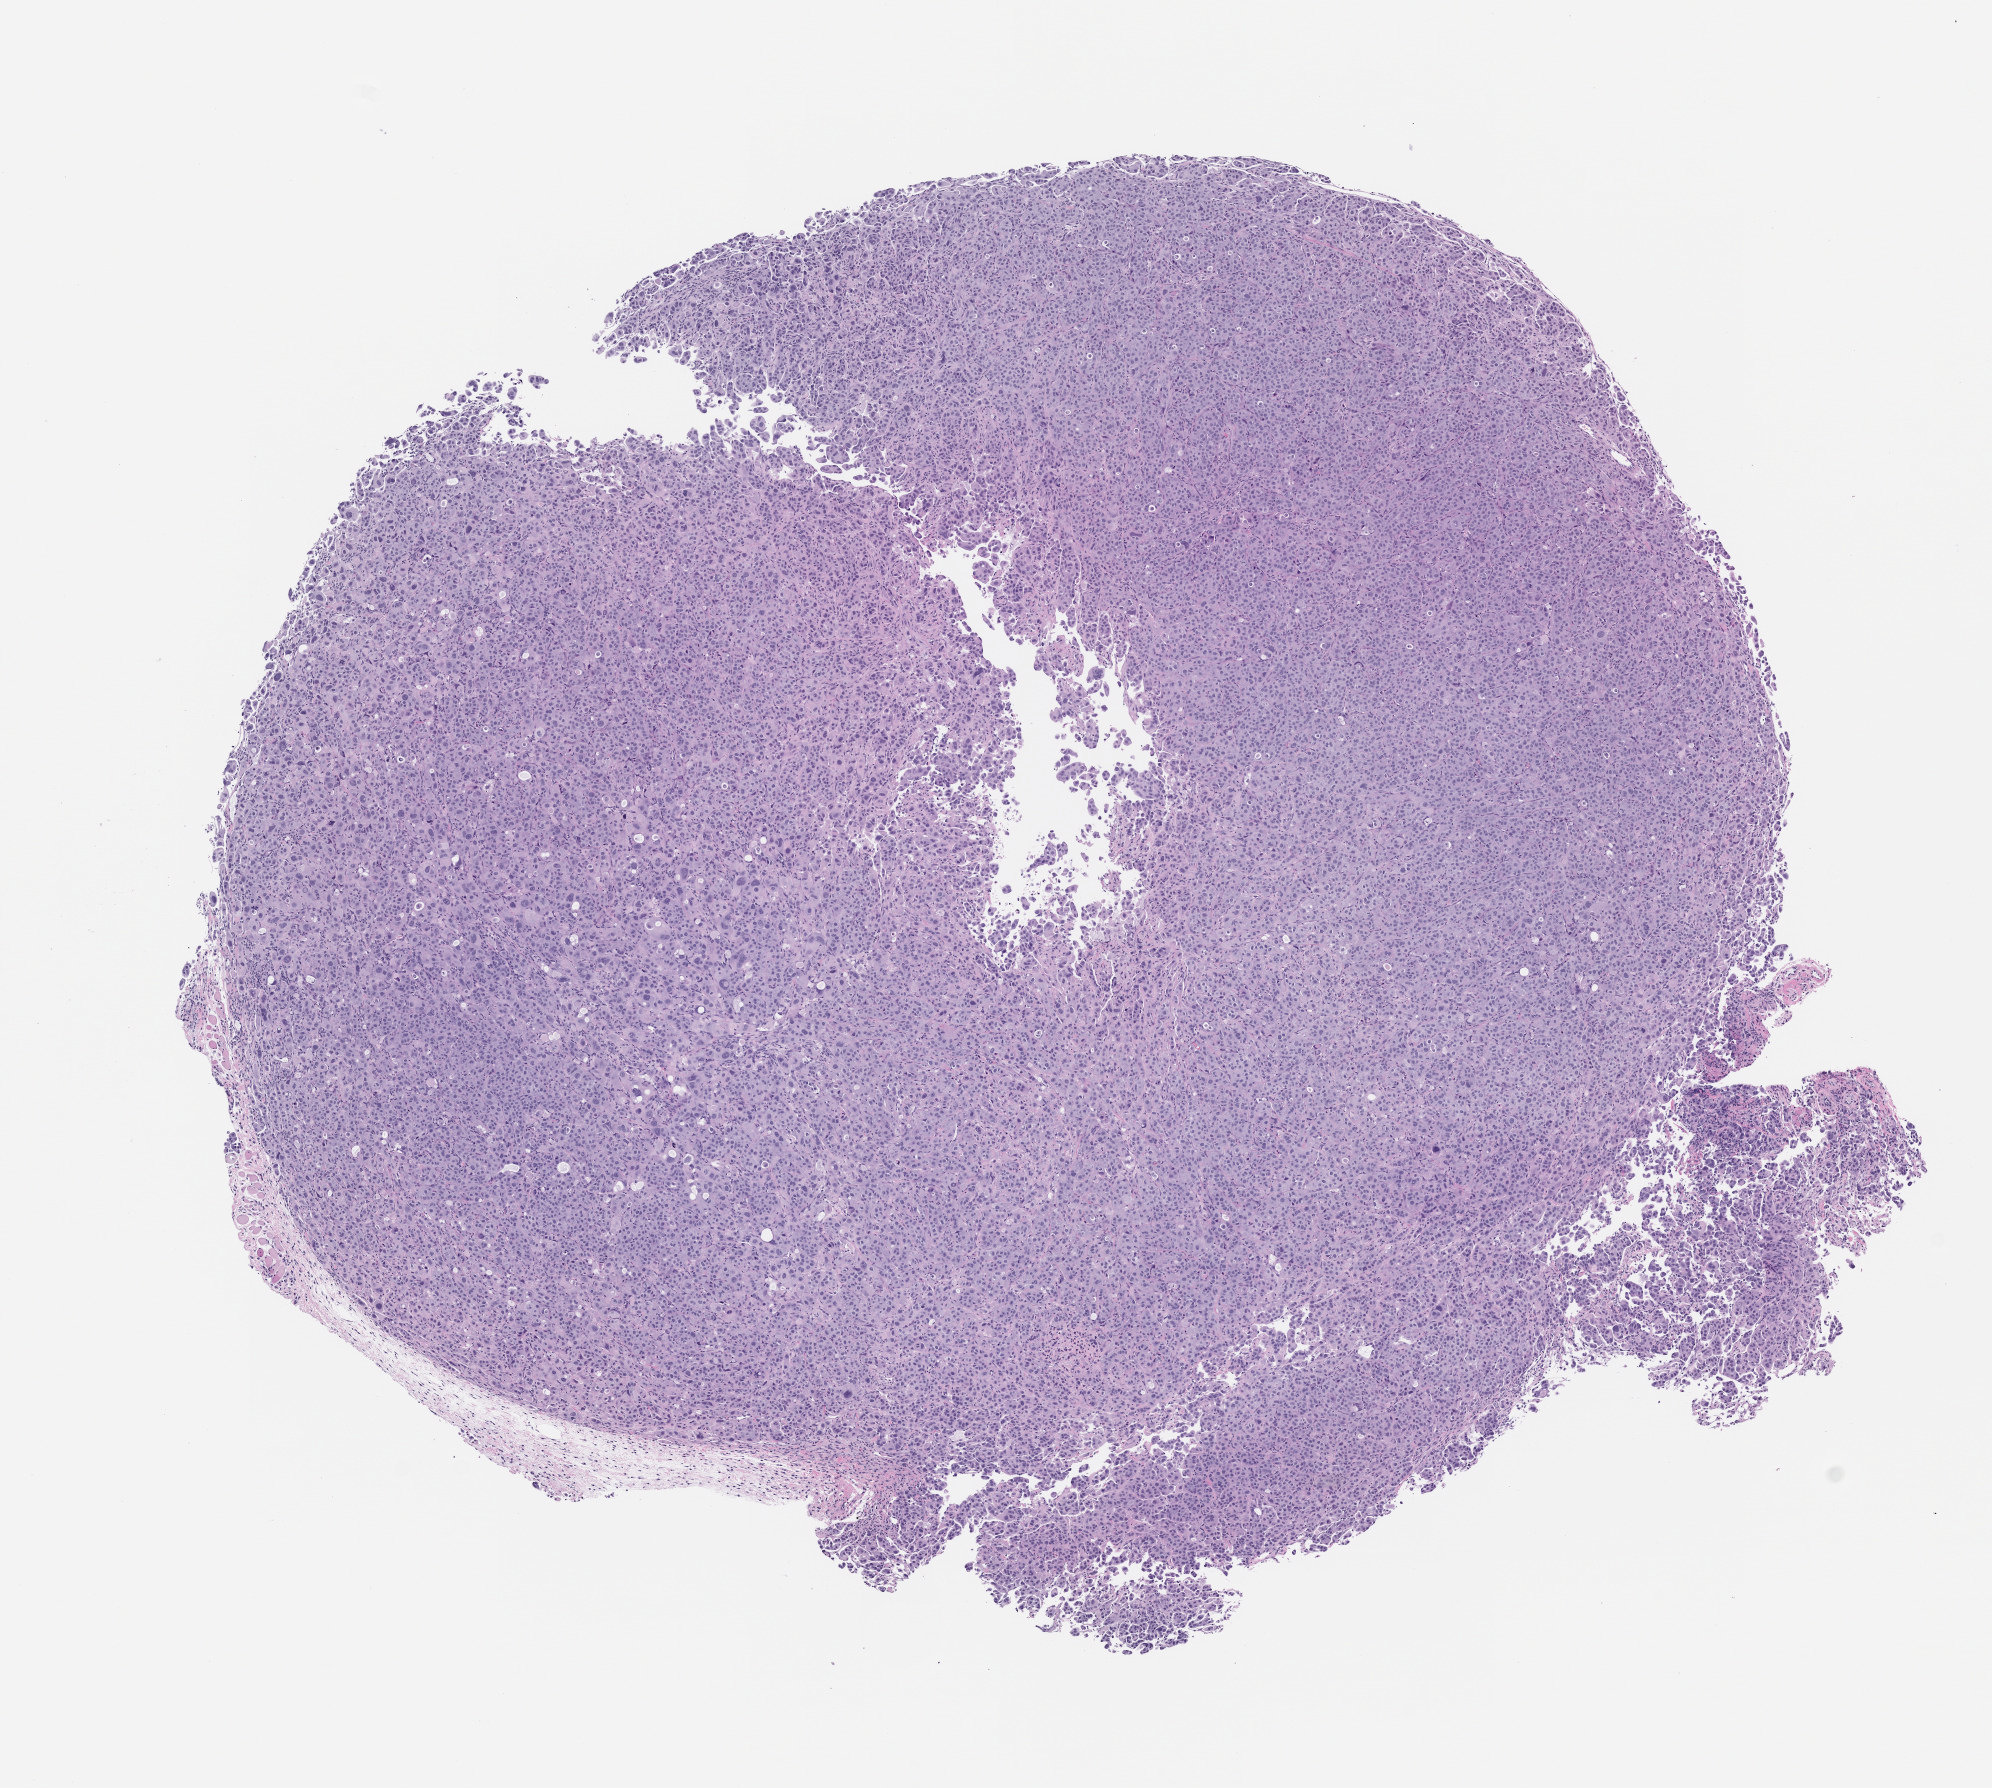
H&E whole-slide image of a patient-derived xenograft (PDX) tumor grown in a mouse — a low-resolution overview of the entire scanned area, about 8.0 x 7.2 mm. FFPE section. Originating tumor site category: lung.
Originating patient diagnosis: Lung Squamous Cell Carcinoma.